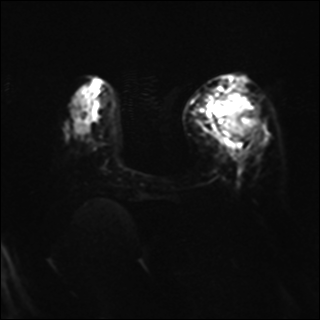
Breast MRI, one axial slice; position 10 of 37 along the scan axis; diffusion-weighted series; image 2 of 4 stored at this slice position (different b-values; order by instance number); 1.5 T; 320 × 320 image matrix. Female patient.
Annotated regions visible in this slice (expert manual segmentation):
- tumour on diffusion-weighted imaging: bounding box (x1, y1, x2, y2) in pixels: (214, 92, 259, 140)